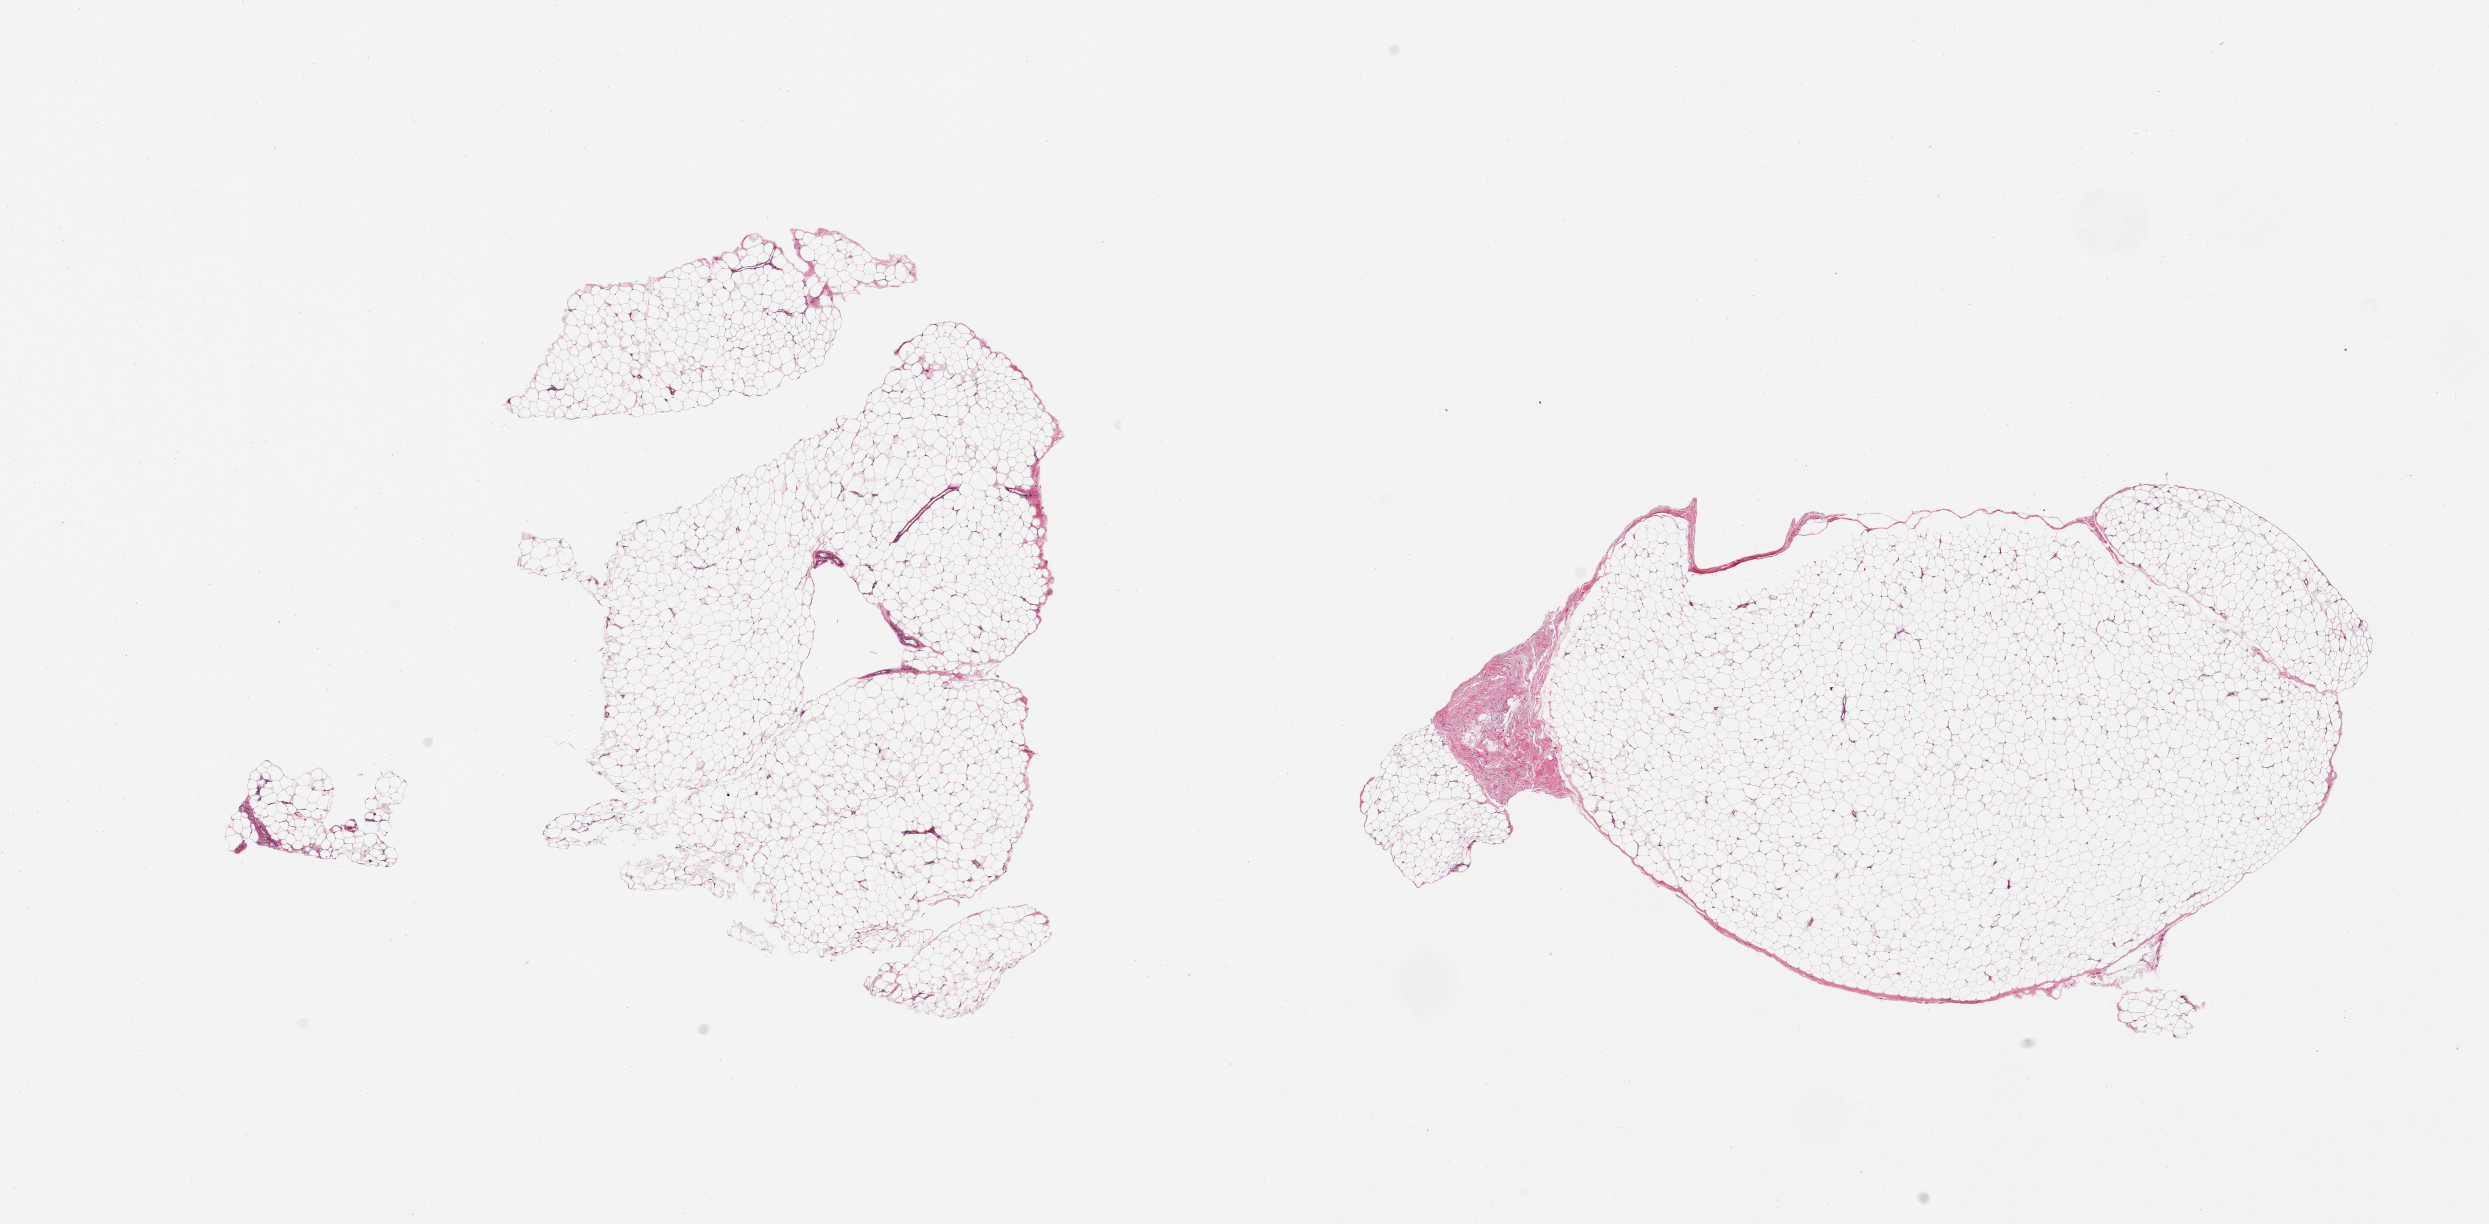
Digitized H&E-stained section — shown as a low-resolution overview of the whole scanned area (about 19.7 x 9.7 mm). PAXgene-fixed, paraffin-embedded tissue. Target tissue: adipose tissue. Tissue donor sample. Female donor.
• reviewer comment on this tissue sample: 2 pieces